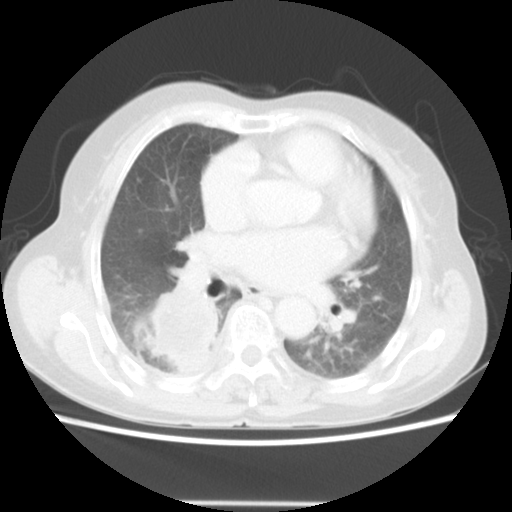
Chest CT, one axial slice. Slice 26 of 52 in the series (ordered by position). Lung window (W 1500 / L -600 HU). 512 × 512 image matrix. Patient: female, 67 years. From the clinical record (not read from this slice): clinical TNM (as recorded): T3 N1 M1.
Outlined on this slice (rectangle marked by the reading radiologist):
- lung tumour (recorded histology: adenocarcinoma): bounding box [x1, y1, x2, y2] px = [135, 284, 222, 372]